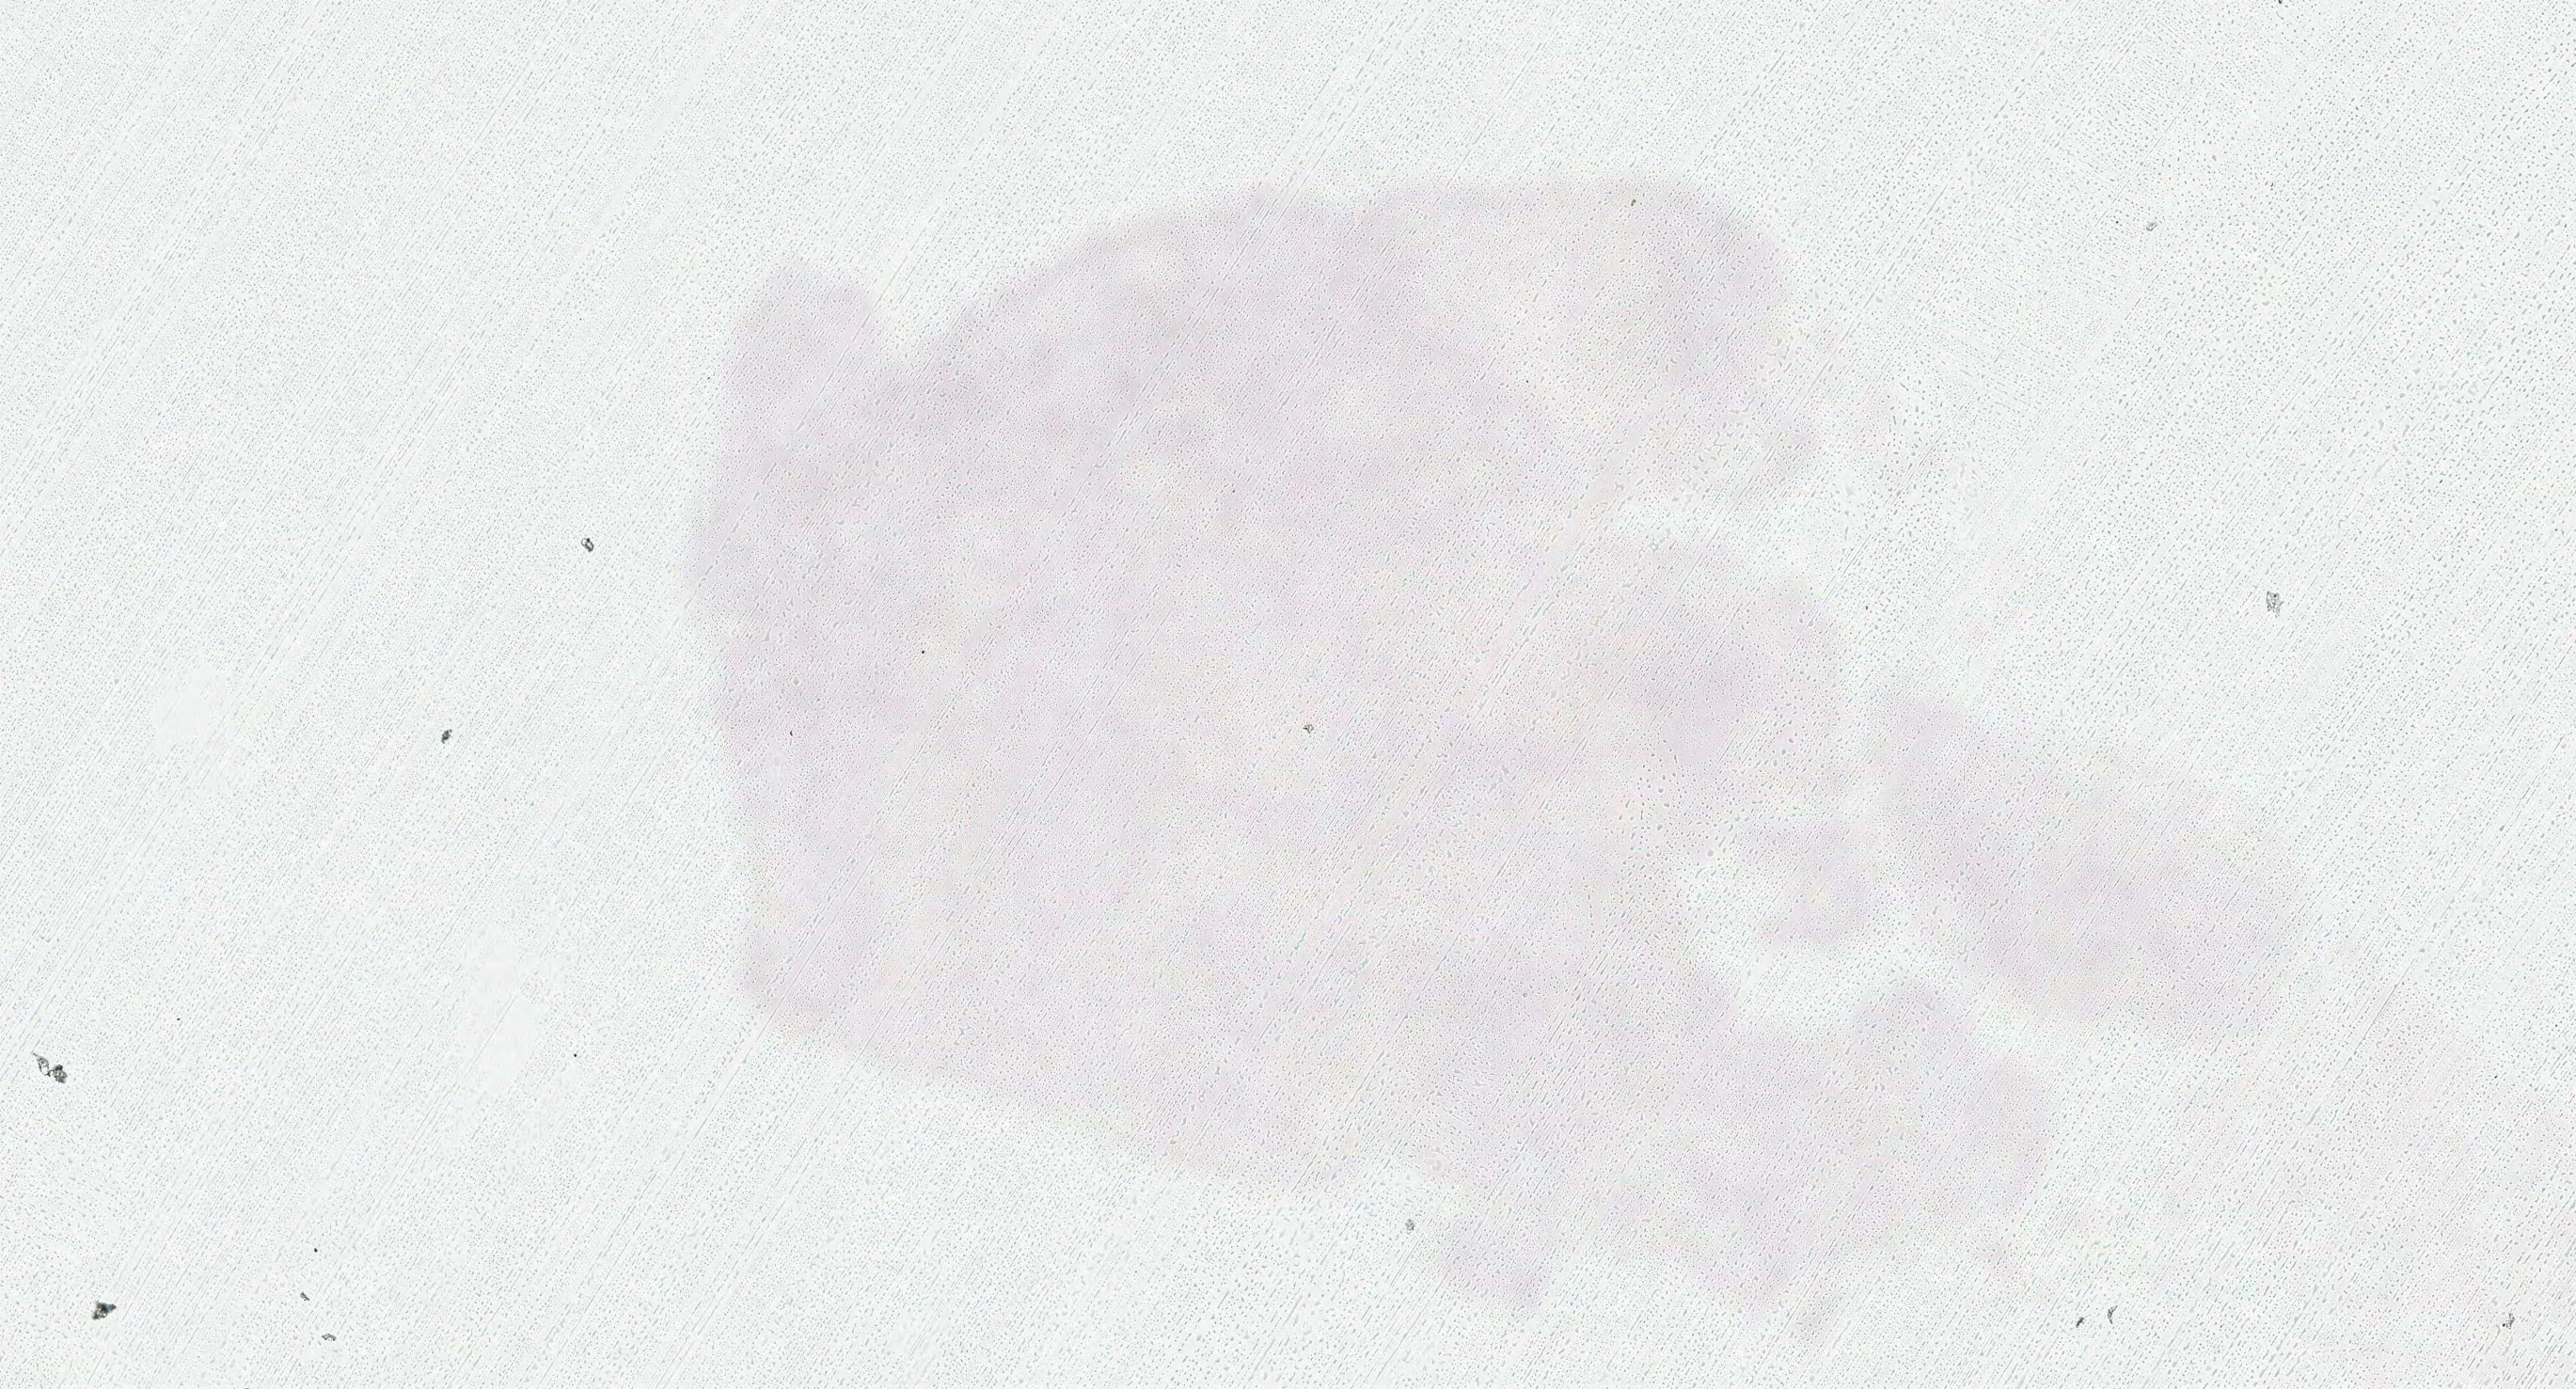
Whole-slide histology image, H&E — shown as a low-resolution overview of the whole scanned area (about 5.4 x 2.9 mm); formalin-fixed paraffin-embedded (FFPE) diagnostic section; brain, primary tumour sample. Male patient; age at initial diagnosis 51 years.
Diagnosis: Glioblastoma.